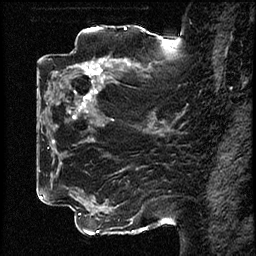
Breast MRI (dynamic contrast-enhanced), one sagittal slice; slice 36 of 78 in the series (ordered by position); dynamic contrast-enhanced study with each time point stored as its own series, time point 2 of 3 at this slice position (early post-contrast, ordered by acquisition time); 1.5 T; TE 4.2 ms, TR 17.6 ms; 256 × 256 image matrix, field of view 200 × 200 mm. Patient: female, 42 years. From the clinical record (not read from this slice): setting: breast cancer imaged before/during neoadjuvant chemotherapy; receptor status: HER2-positive.
Structures marked on this image (semi-automatic segmentation, software-assisted and operator-edited):
- analysis volume of interest (the breast-tissue region the enhancement analysis was run in; not a lesion): box from (x=50, y=48) to (x=131, y=129) px
- tumour enhancement mask (voxels above the 100 % enhancement threshold inside the analysis volume of interest): (x=73, y=60)–(x=118, y=118)